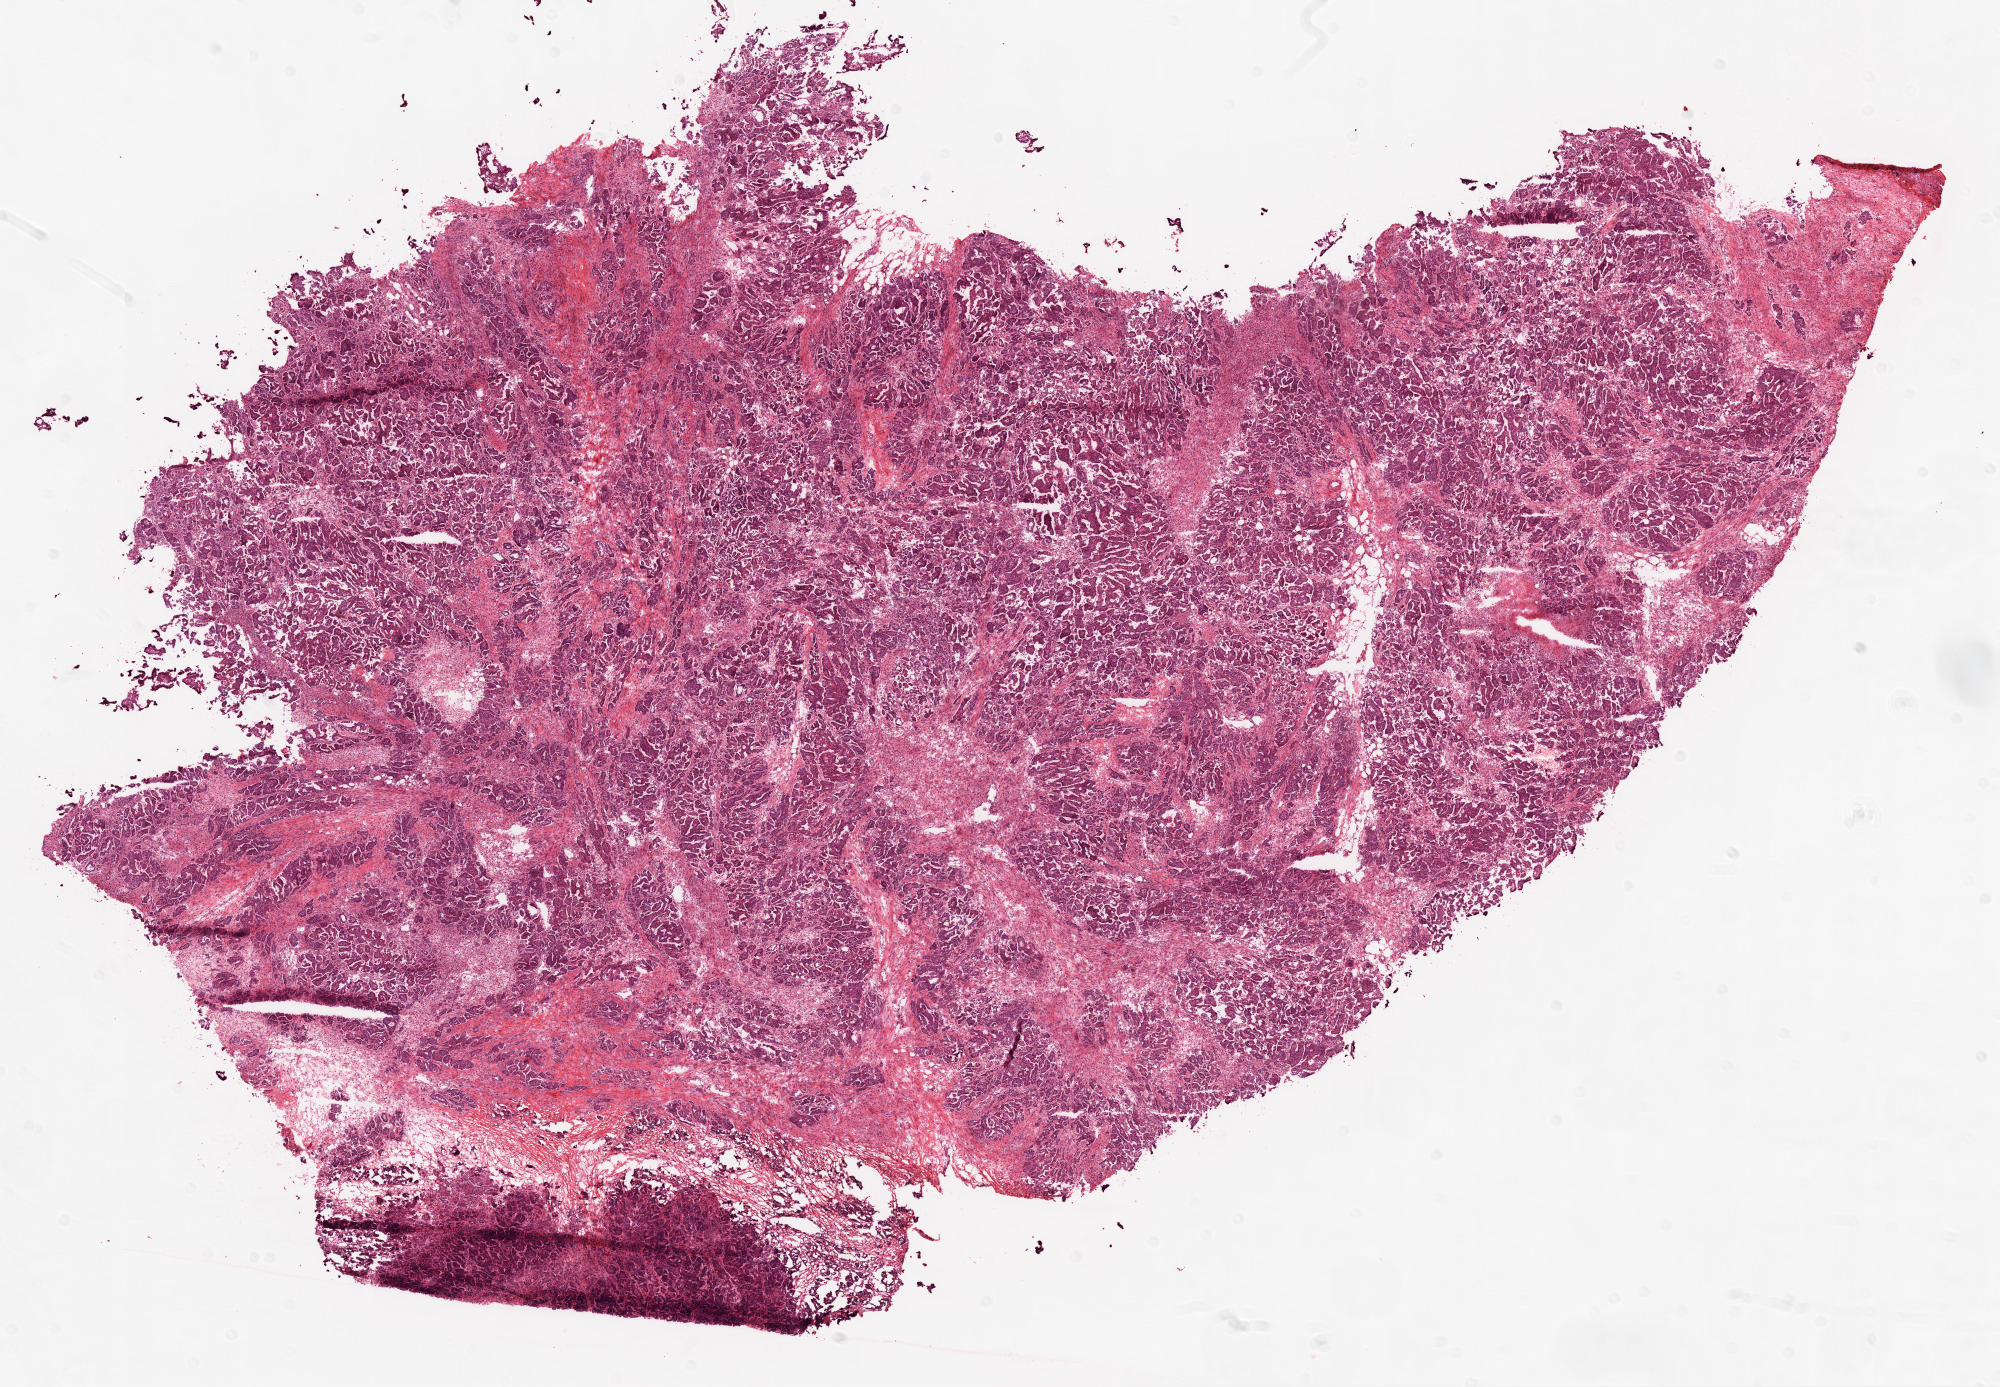
Whole-slide histology image, H&E, a low-resolution overview of the entire scanned area, about 16.0 x 11.1 mm; frozen section; primary tumour sample from the ovary. Female patient; age at initial diagnosis 47 years. Histologic grade: G2 (moderately differentiated). Pathologist review of this section (percent, as recorded): tumour cells 98%, tumour nuclei 85%, normal cells 0%, stromal cells 0%, necrosis 2%.
- FIGO stage: IIIC
- diagnosis: Serous cystadenocarcinoma, NOS